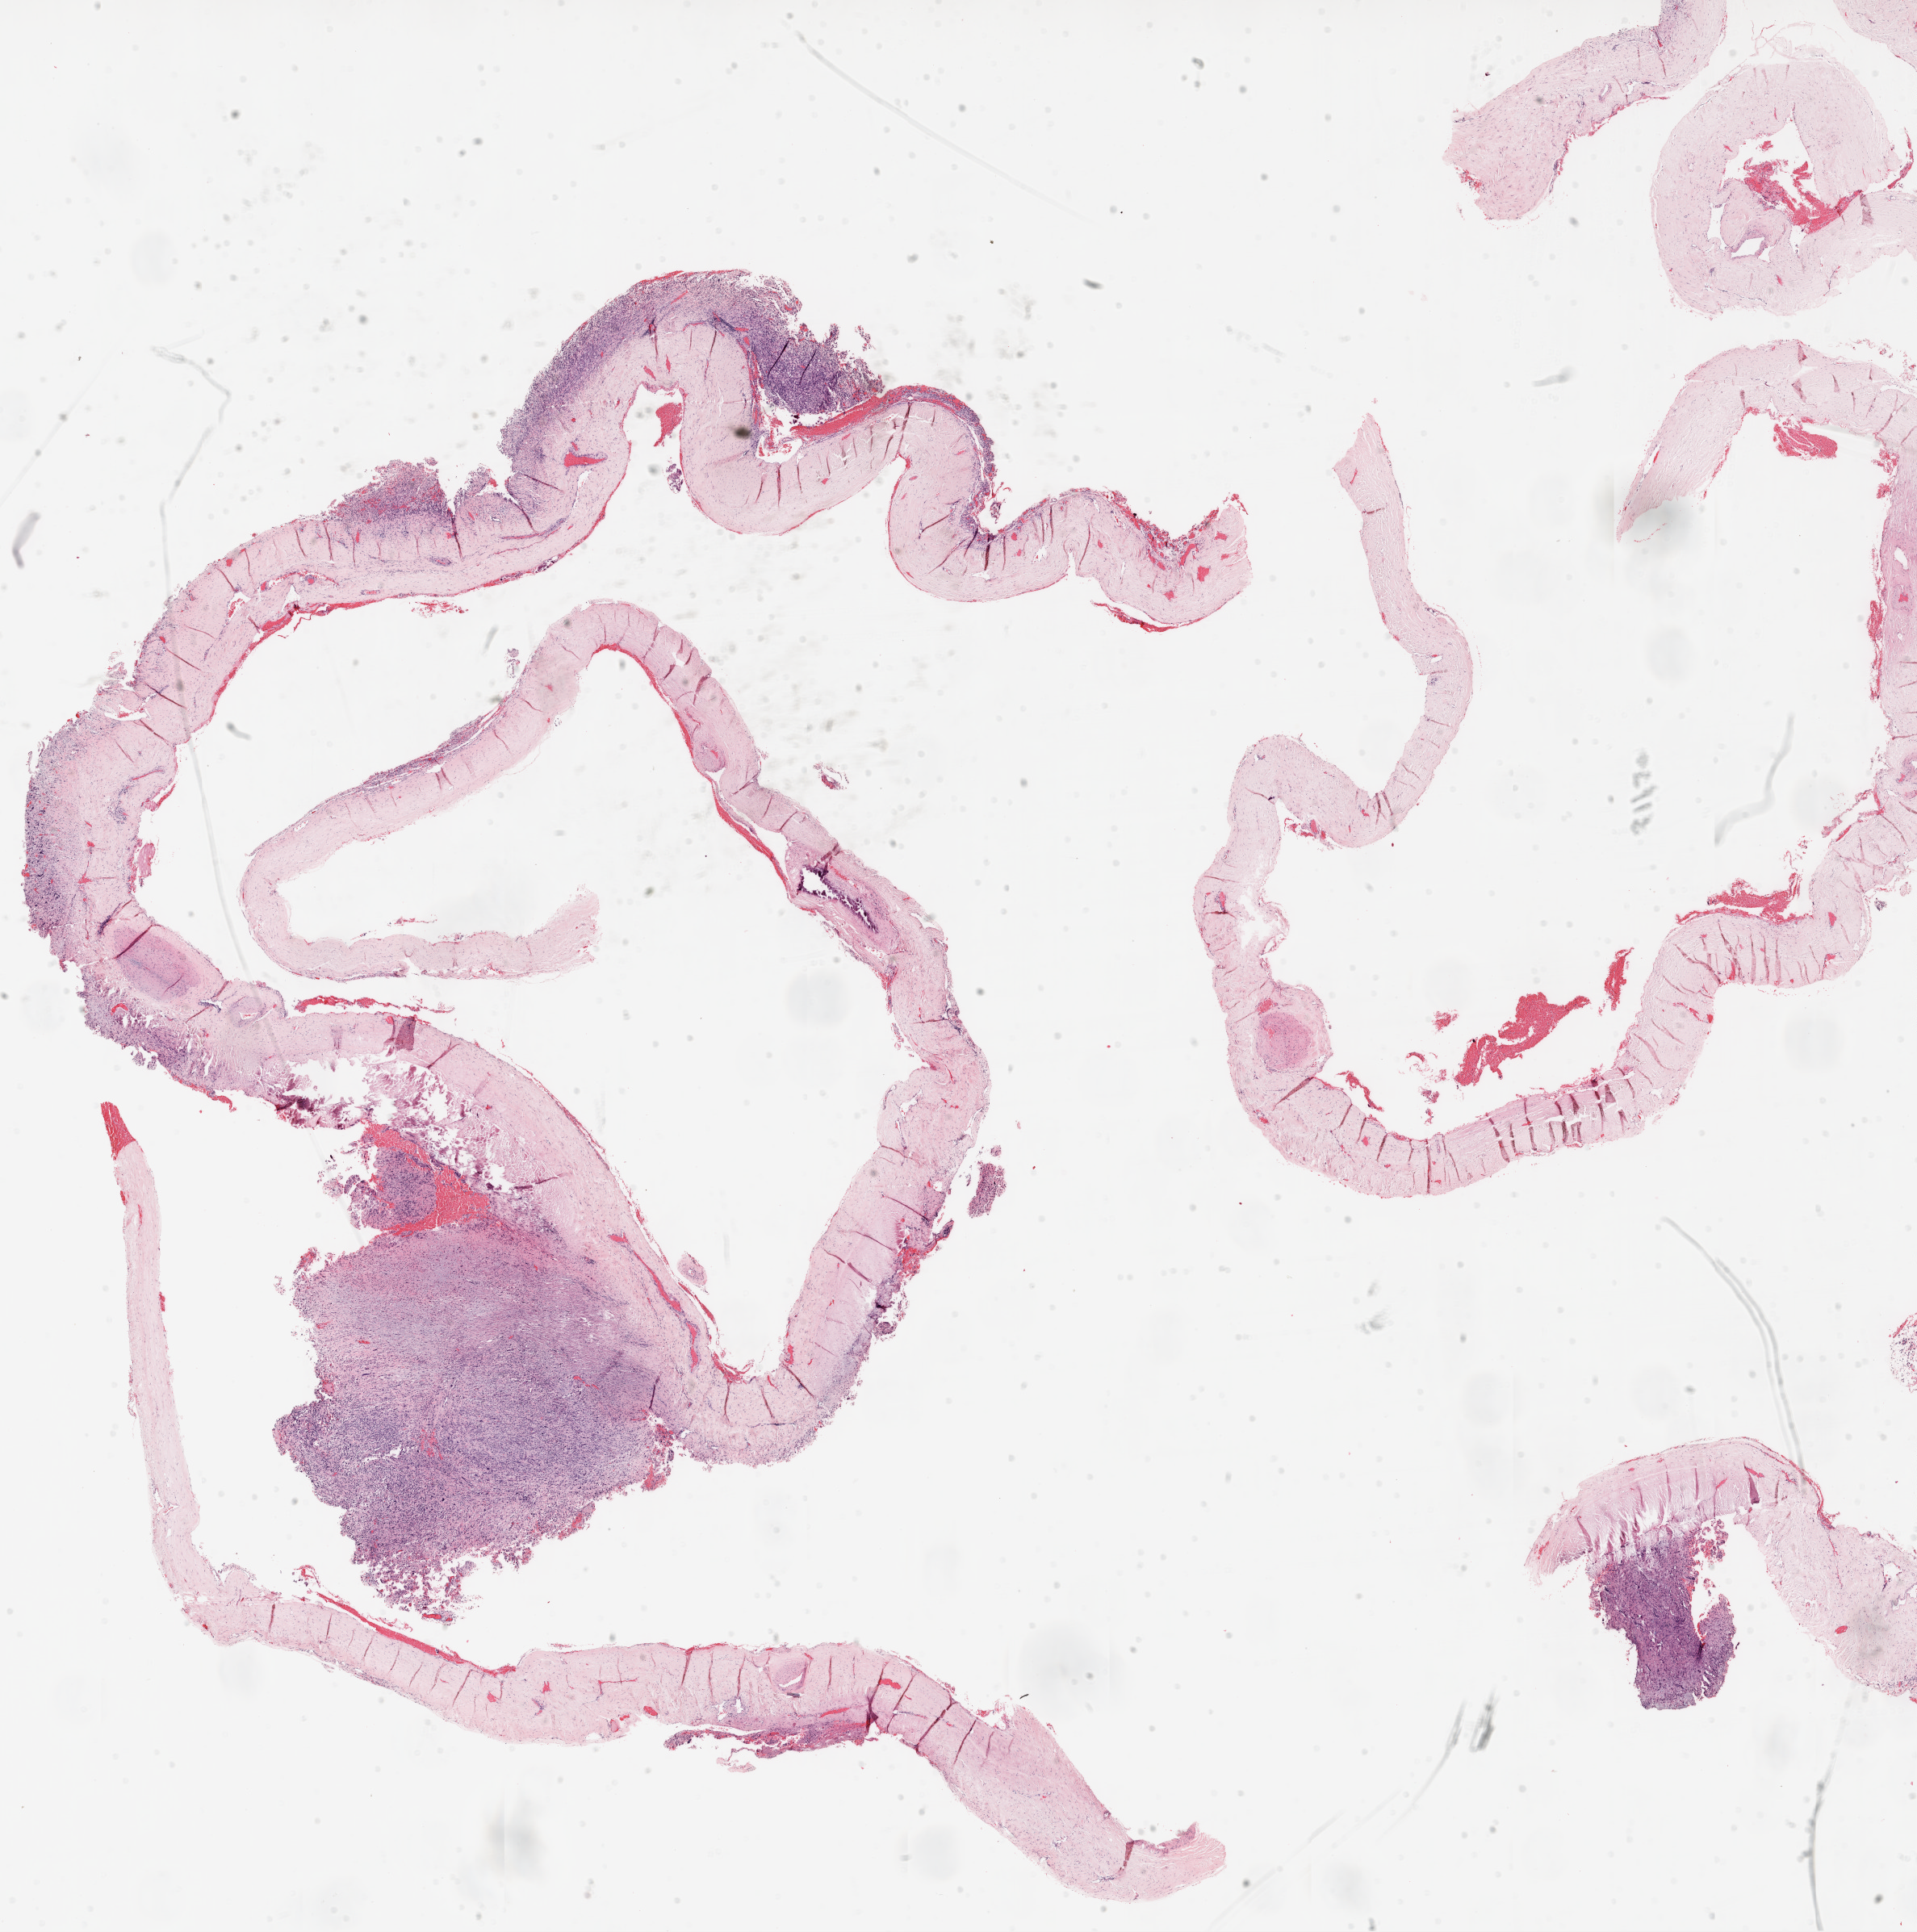
H&E whole-slide image — a low-resolution overview of the entire scanned area, about 19.1 x 19.2 mm (from a 20x scan); formalin-fixed paraffin-embedded (FFPE) diagnostic section; sample: primary tumour, brain. Female patient; age at initial diagnosis 60 years.
Pathologic diagnosis: Glioblastoma.